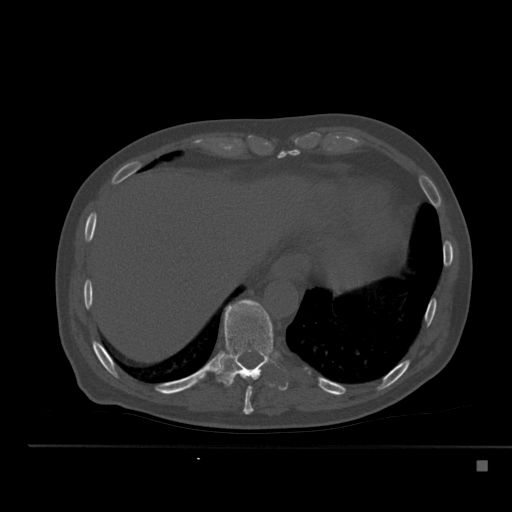
CT including the spine, one axial slice; position 272 of 517 along the scan axis; reconstruction kernel Br40s; 120 kVp; bone window (W 1800 / L 400 HU); 1.5 mm slice thickness; 512 × 512 image matrix, field of view 408 × 408 mm. Patient: male, 70 years. Case-level facts recorded for this patient, not image findings: primary cancer: renal; vertebrae with lytic lesions (as recorded): T4, T6, T10, T12, L3, L4, L5.
Outlined on this slice (semi-automatic segmentation, software-assisted and operator-edited):
- T10 vertebra: bounding box [x1, y1, x2, y2] px = [217, 299, 273, 387]
- T9 vertebra: [243, 386, 253, 415]